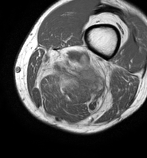
MRI of an extremity soft-tissue mass, one axial slice. Slice 23 of 86 in the series (ordered by position). MR volume resampled by the dataset authors to the PET/CT grid (not the native acquisition matrix). 147 × 158 image matrix, field of view 144 × 154 mm. Male patient. Case-level facts recorded for this patient, not image findings: histological type: undifferentiated pleomorphic liposarcoma; grade: high; site of the primary tumour: left thigh.
Structures marked on this image (expert contour drawn on MRI and transferred to this co-registered scan by the dataset authors):
- gross tumour volume including surrounding oedema: bounding box [x1, y1, x2, y2] px = [35, 44, 116, 121]